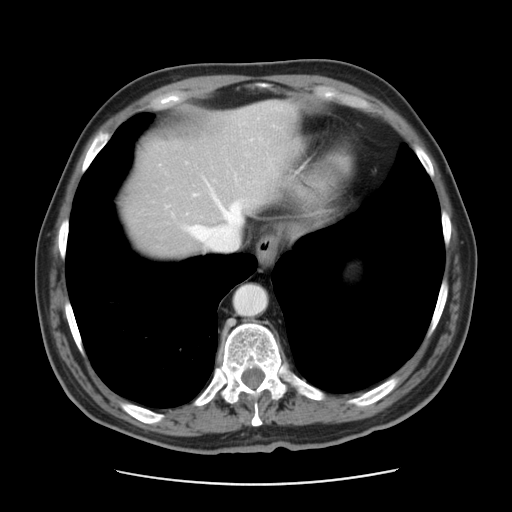
Contrast-enhanced abdominal CT, one axial slice; 120 kVp; intravenous contrast given; soft-tissue window (W 400 / L 40 HU); 512 × 512 image matrix. Male patient, age 73 years. Case-level facts recorded for this patient, not image findings: diagnosis: colorectal cancer liver metastases, imaged before liver resection; multiple liver metastases: yes; largest metastasis: 0.5 cm.
Annotated regions visible in this slice (outlined manually by an expert reader):
- hepatic veins: bounding box <164,174,247,250> (left, top, right, bottom; pixels)
- liver: <127,102,293,255>
- planned liver remnant (the part of the liver to remain after resection): <146,102,293,225>